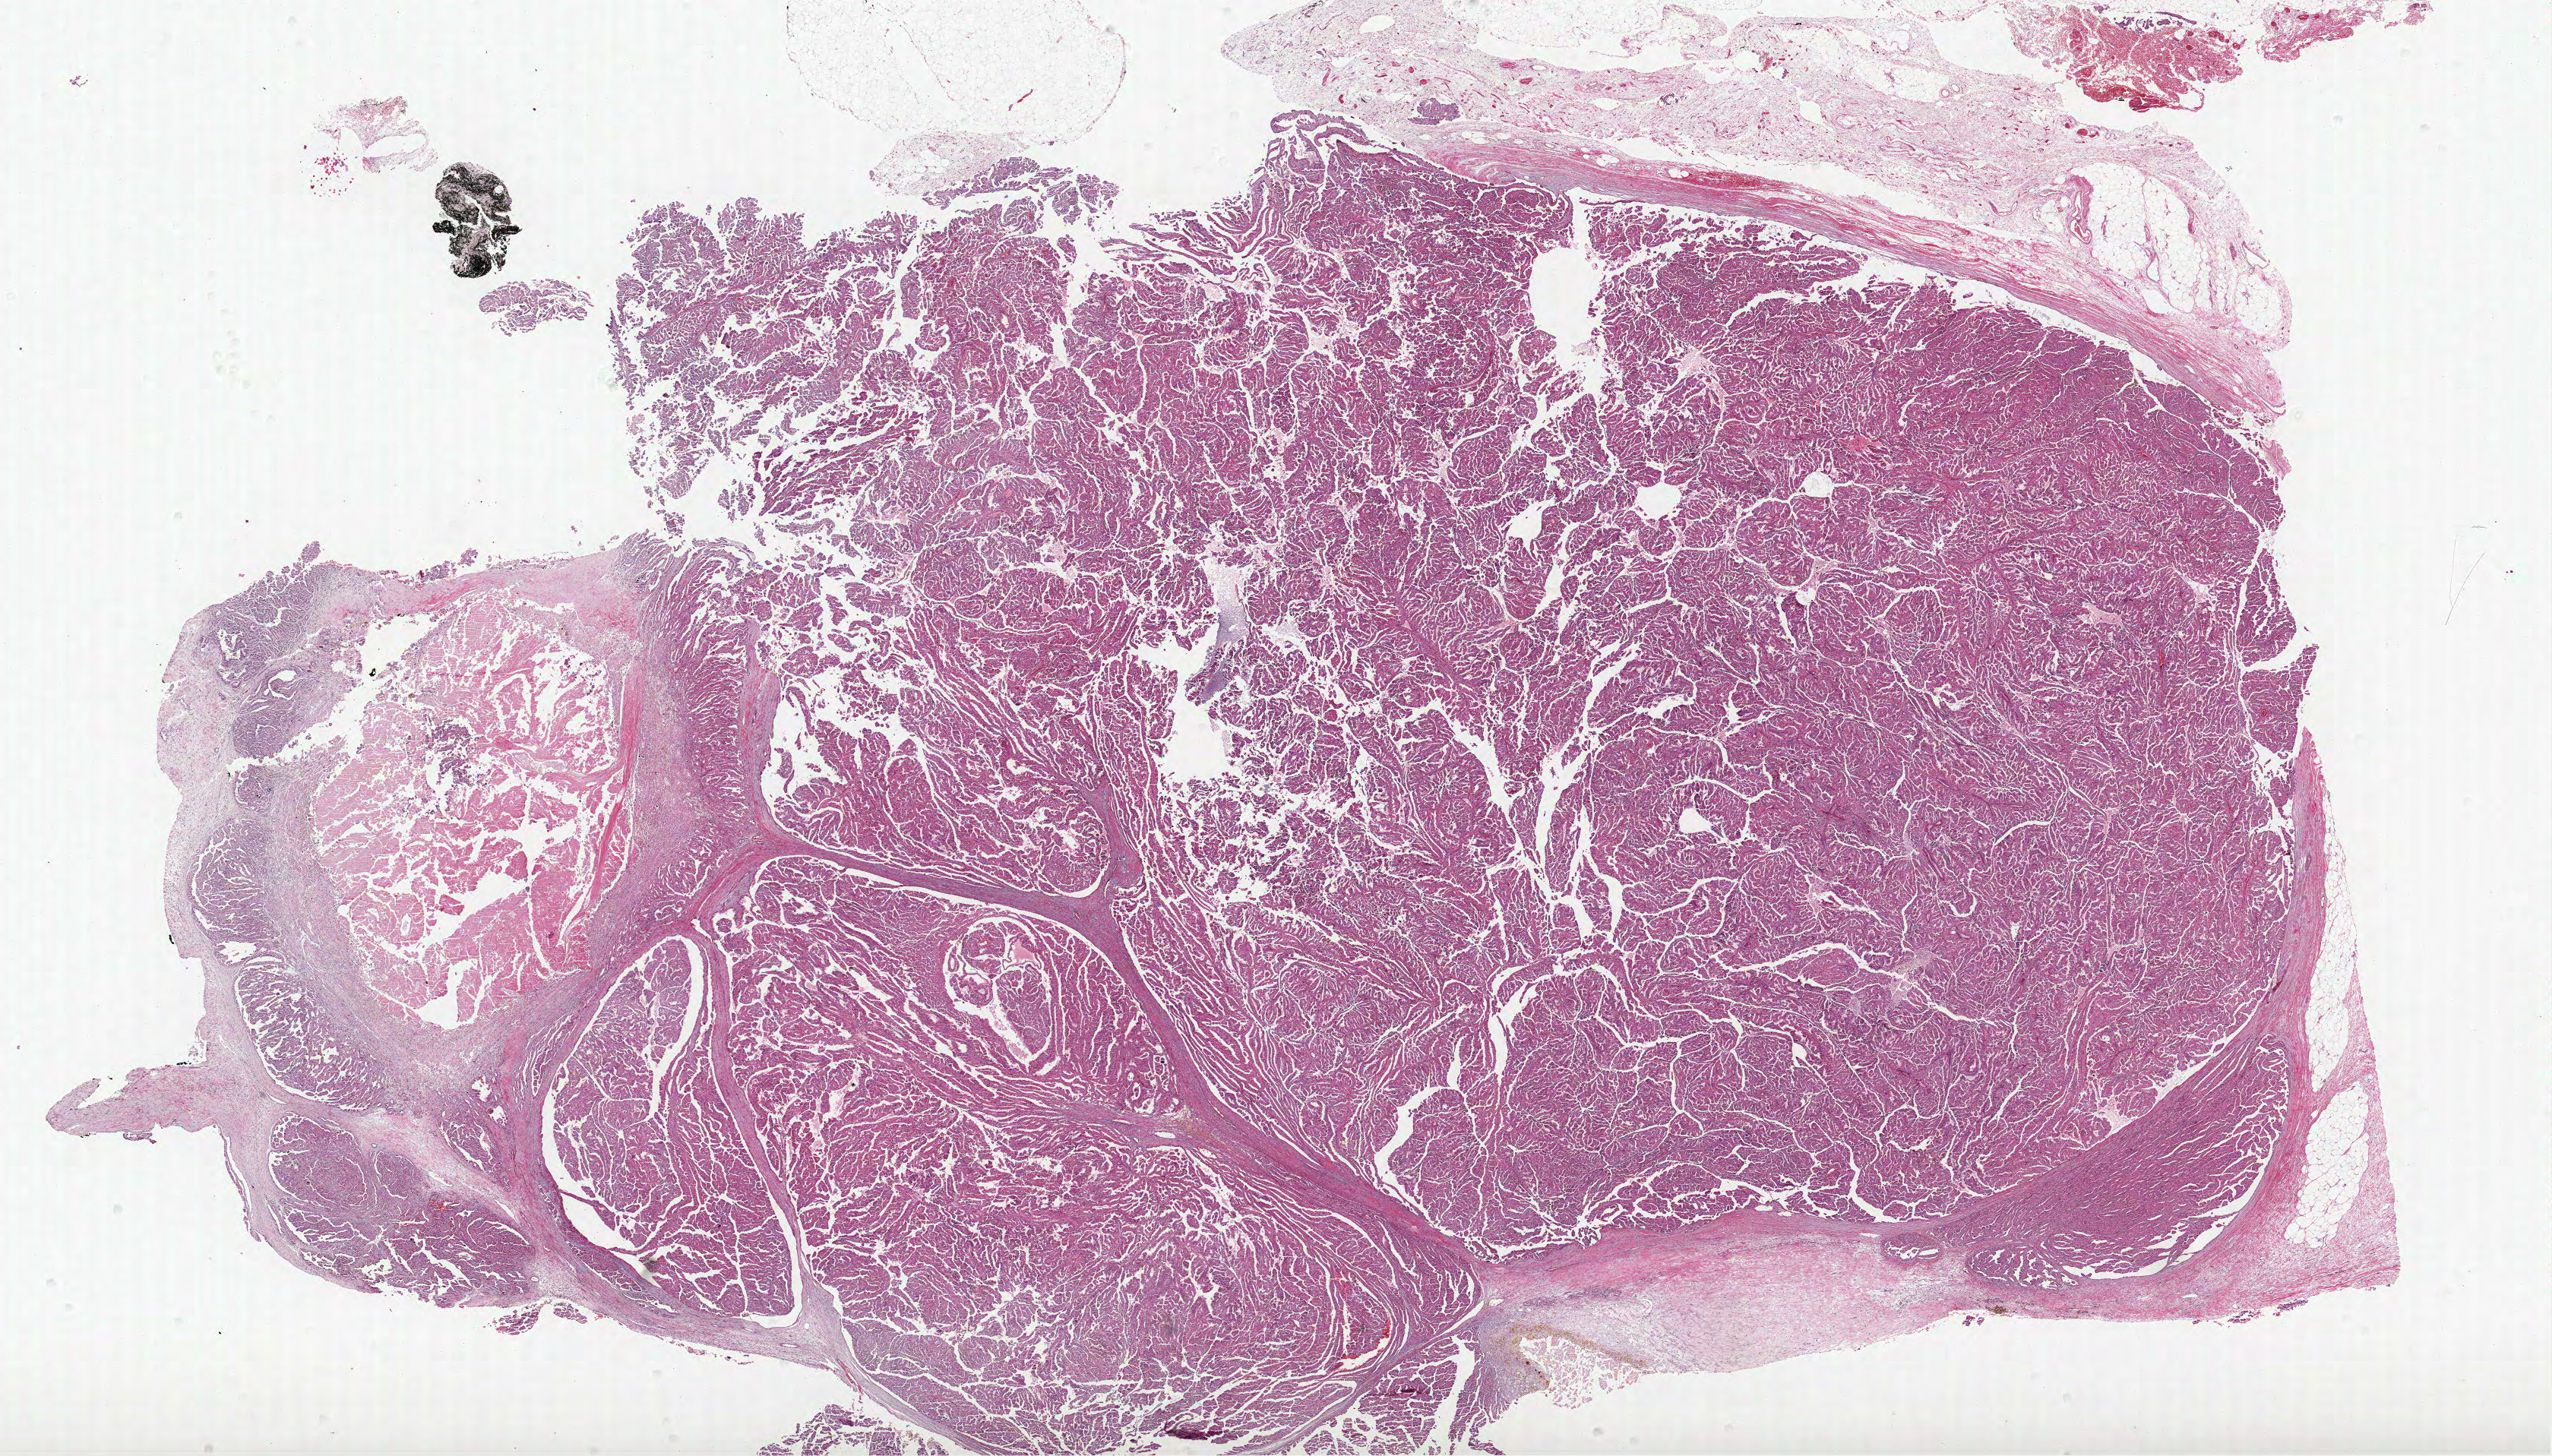
Digitized H&E tissue section (whole slide), low-resolution overview of the scanned area, about 26.9 x 15.3 mm (slide scanned at 40x); formalin-fixed paraffin-embedded (FFPE) diagnostic section; kidney, primary tumour sample. Patient: female, age at initial diagnosis 79 years.
- AJCC pathologic stage: III
- histologic diagnosis: Papillary adenocarcinoma, NOS
- laterality: left